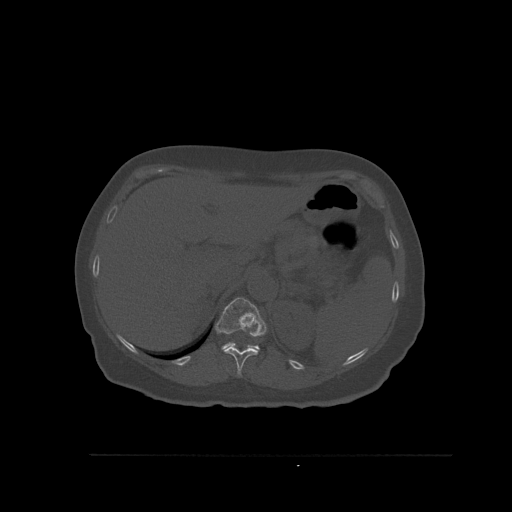
CT including the spine, one axial slice; slice 295 of 527 in the series (ordered by position); bone window (W 1800 / L 400 HU); 512 × 512 image matrix. Female patient, age 73 years. From the clinical record (not read from this slice): primary cancer: breast; vertebrae with lytic lesions (as recorded): L2.
Outlined on this slice (semi-automatic segmentation, software-assisted and operator-edited):
- T11 vertebra: bounding box <222,347,259,377> (left, top, right, bottom; pixels)
- T12 vertebra: <215,297,267,350>